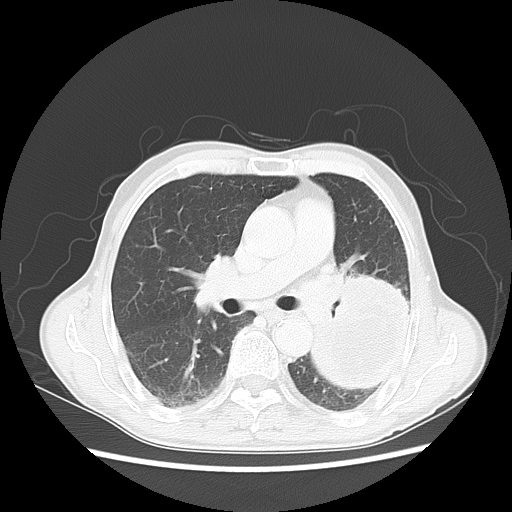
Chest CT, one axial slice; position 30 of 51 along the scan axis; lung window (W 1500 / L -600 HU); 512 × 512 image matrix, field of view 360 × 360 mm. Patient: male, 64 years. From the clinical record (not read from this slice): clinical TNM (as recorded): T4 N0 M0.
Structures marked on this image (bounding box drawn by a radiologist):
- lung tumour (recorded histology: squamous cell carcinoma): bounding box (x1, y1, x2, y2) in pixels: (307, 266, 413, 389)